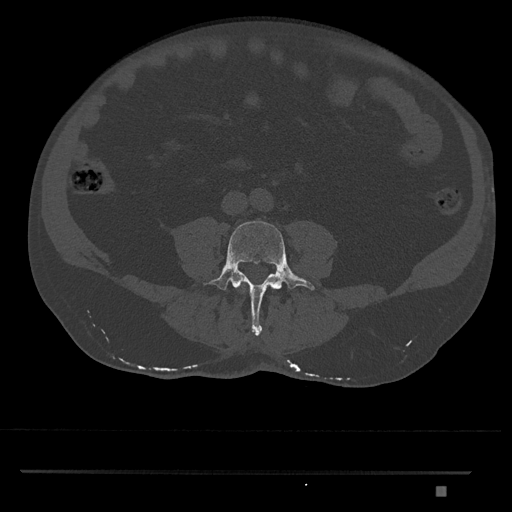
CT including the spine, one axial slice; position 620 of 1134 along the scan axis; 120 kVp; bone window (W 1800 / L 400 HU); 0.5 mm slice thickness; 512 × 512 image matrix, field of view 429 × 429 mm. Male patient, age 65 years. From the clinical record (not read from this slice): primary cancer: prostate.
Structures marked on this image (semi-automatically segmented with operator editing):
- L3 vertebra: bounding box [x1, y1, x2, y2] px = [242, 289, 244, 291]
- L4 vertebra: [203, 221, 315, 336]